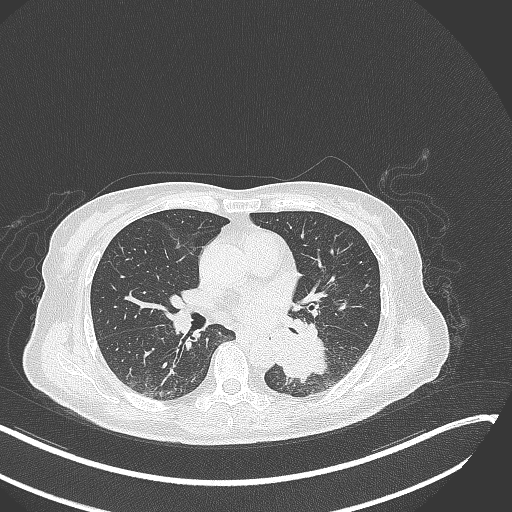
Chest CT, one axial slice; position 140 of 342 along the scan axis; 120 kVp; lung window (W 1500 / L -600 HU); 1 mm slice thickness; 512 × 512 image matrix, field of view 400 × 400 mm. Patient: female, 64 years. From the clinical record (not read from this slice): clinical TNM (as recorded): T3 N1 M1.
Annotated regions visible in this slice (bounding box drawn by a radiologist):
- lung tumour (recorded histology: small cell carcinoma): bounding box <267,328,333,386> (left, top, right, bottom; pixels)